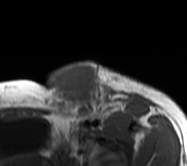
MRI of an extremity soft-tissue mass, one axial slice. Slice 44 of 62 in the series (ordered by position). MR volume resampled by the dataset authors to the PET/CT grid (not the native acquisition matrix). 187 × 166 image matrix. Female patient. From the clinical record (not read from this slice): histological type: leiomyosarcoma; grade: high; site of the primary tumour: groin.
Annotated regions visible in this slice (expert contour drawn on MRI and transferred to this co-registered scan by the dataset authors):
- gross tumour volume including surrounding oedema: bounding box <46,62,154,127> (left, top, right, bottom; pixels)
- gross tumour volume (mass): <48,62,106,118>